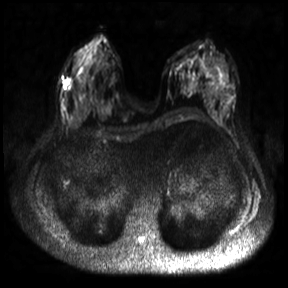
Breast MRI, one axial slice. Position 13 of 30 along the scan axis. Diffusion-weighted series; image 2 of 4 stored at this slice position (different b-values; order by instance number). 3 T. 288 × 288 image matrix, field of view 360 × 360 mm. Female patient.
Annotated regions visible in this slice (manually delineated by an expert):
- tumour on diffusion-weighted imaging: bounding box [x1, y1, x2, y2] px = [68, 78, 72, 87]